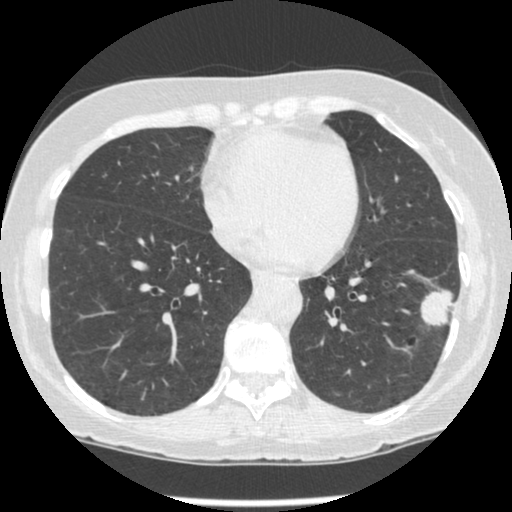
Low-dose screening chest CT, one axial slice. Position 94 of 247 along the scan axis. Reconstruction kernel STANDARD. 120 kVp. Lung window (W 1500 / L -600 HU). 512 × 512 image matrix, field of view 303 × 303 mm.
Outlined on this slice (expert manual segmentation):
- lesion 1 (tumor, lower lobe of left lung): box from (x=420, y=289) to (x=455, y=326) px